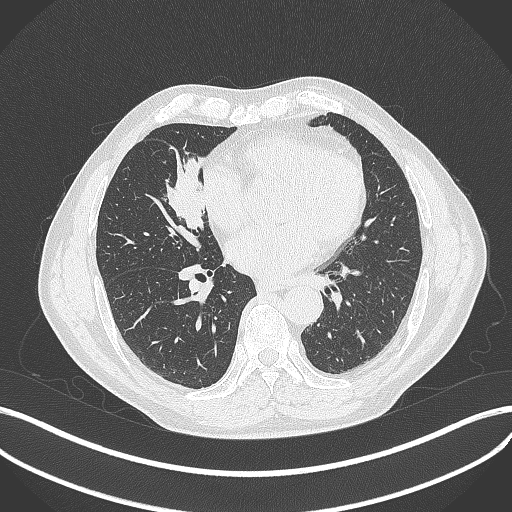
Chest CT, one axial slice. Slice 174 of 429 in the series (ordered by position). Reconstruction kernel B70f. 120 kVp. Lung window (W 1500 / L -600 HU). 1 mm slice thickness. 512 × 512 image matrix, field of view 400 × 400 mm. Male patient, age 61 years. From the clinical record (not read from this slice): clinical TNM (as recorded): T2b N1 M0.
Annotated regions visible in this slice (rectangle marked by the reading radiologist):
- lung tumour (recorded histology: squamous cell carcinoma): box from (x=165, y=157) to (x=212, y=239) px